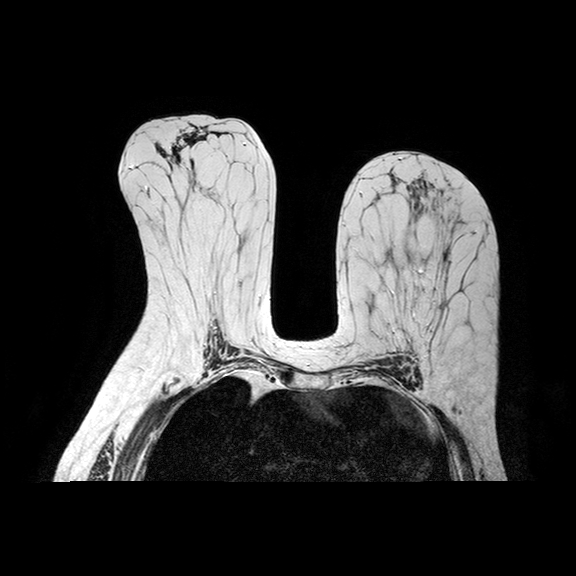
Breast MRI examination; 2 images, each one mid-volume slice chosen by position.
Image 1: fluid-sensitive (T2/STIR) axial slice, series "T2W_TSE SENSE", slice 44 of 86, 2 mm slice thickness.
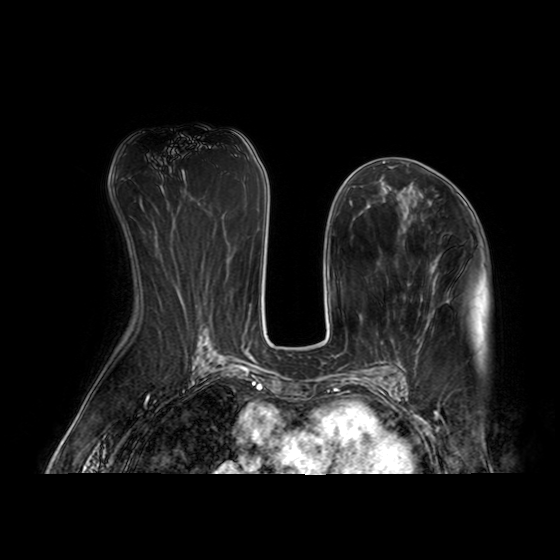
Image 2: post-contrast dynamic axial slice, series "AX BLISS_AUTO SENSE", slice 44 of 86, dynamic phase 5 of 8, 4 mm slice thickness.
Pathology recorded for this patient (not read from these images): pathology diagnosis: ductal CA in situ (left breast); receptor status (as recorded): ER pos, PR pos, HER2 neg; pathology report notes: re-bx [date] at calcific shows no residual tumor.